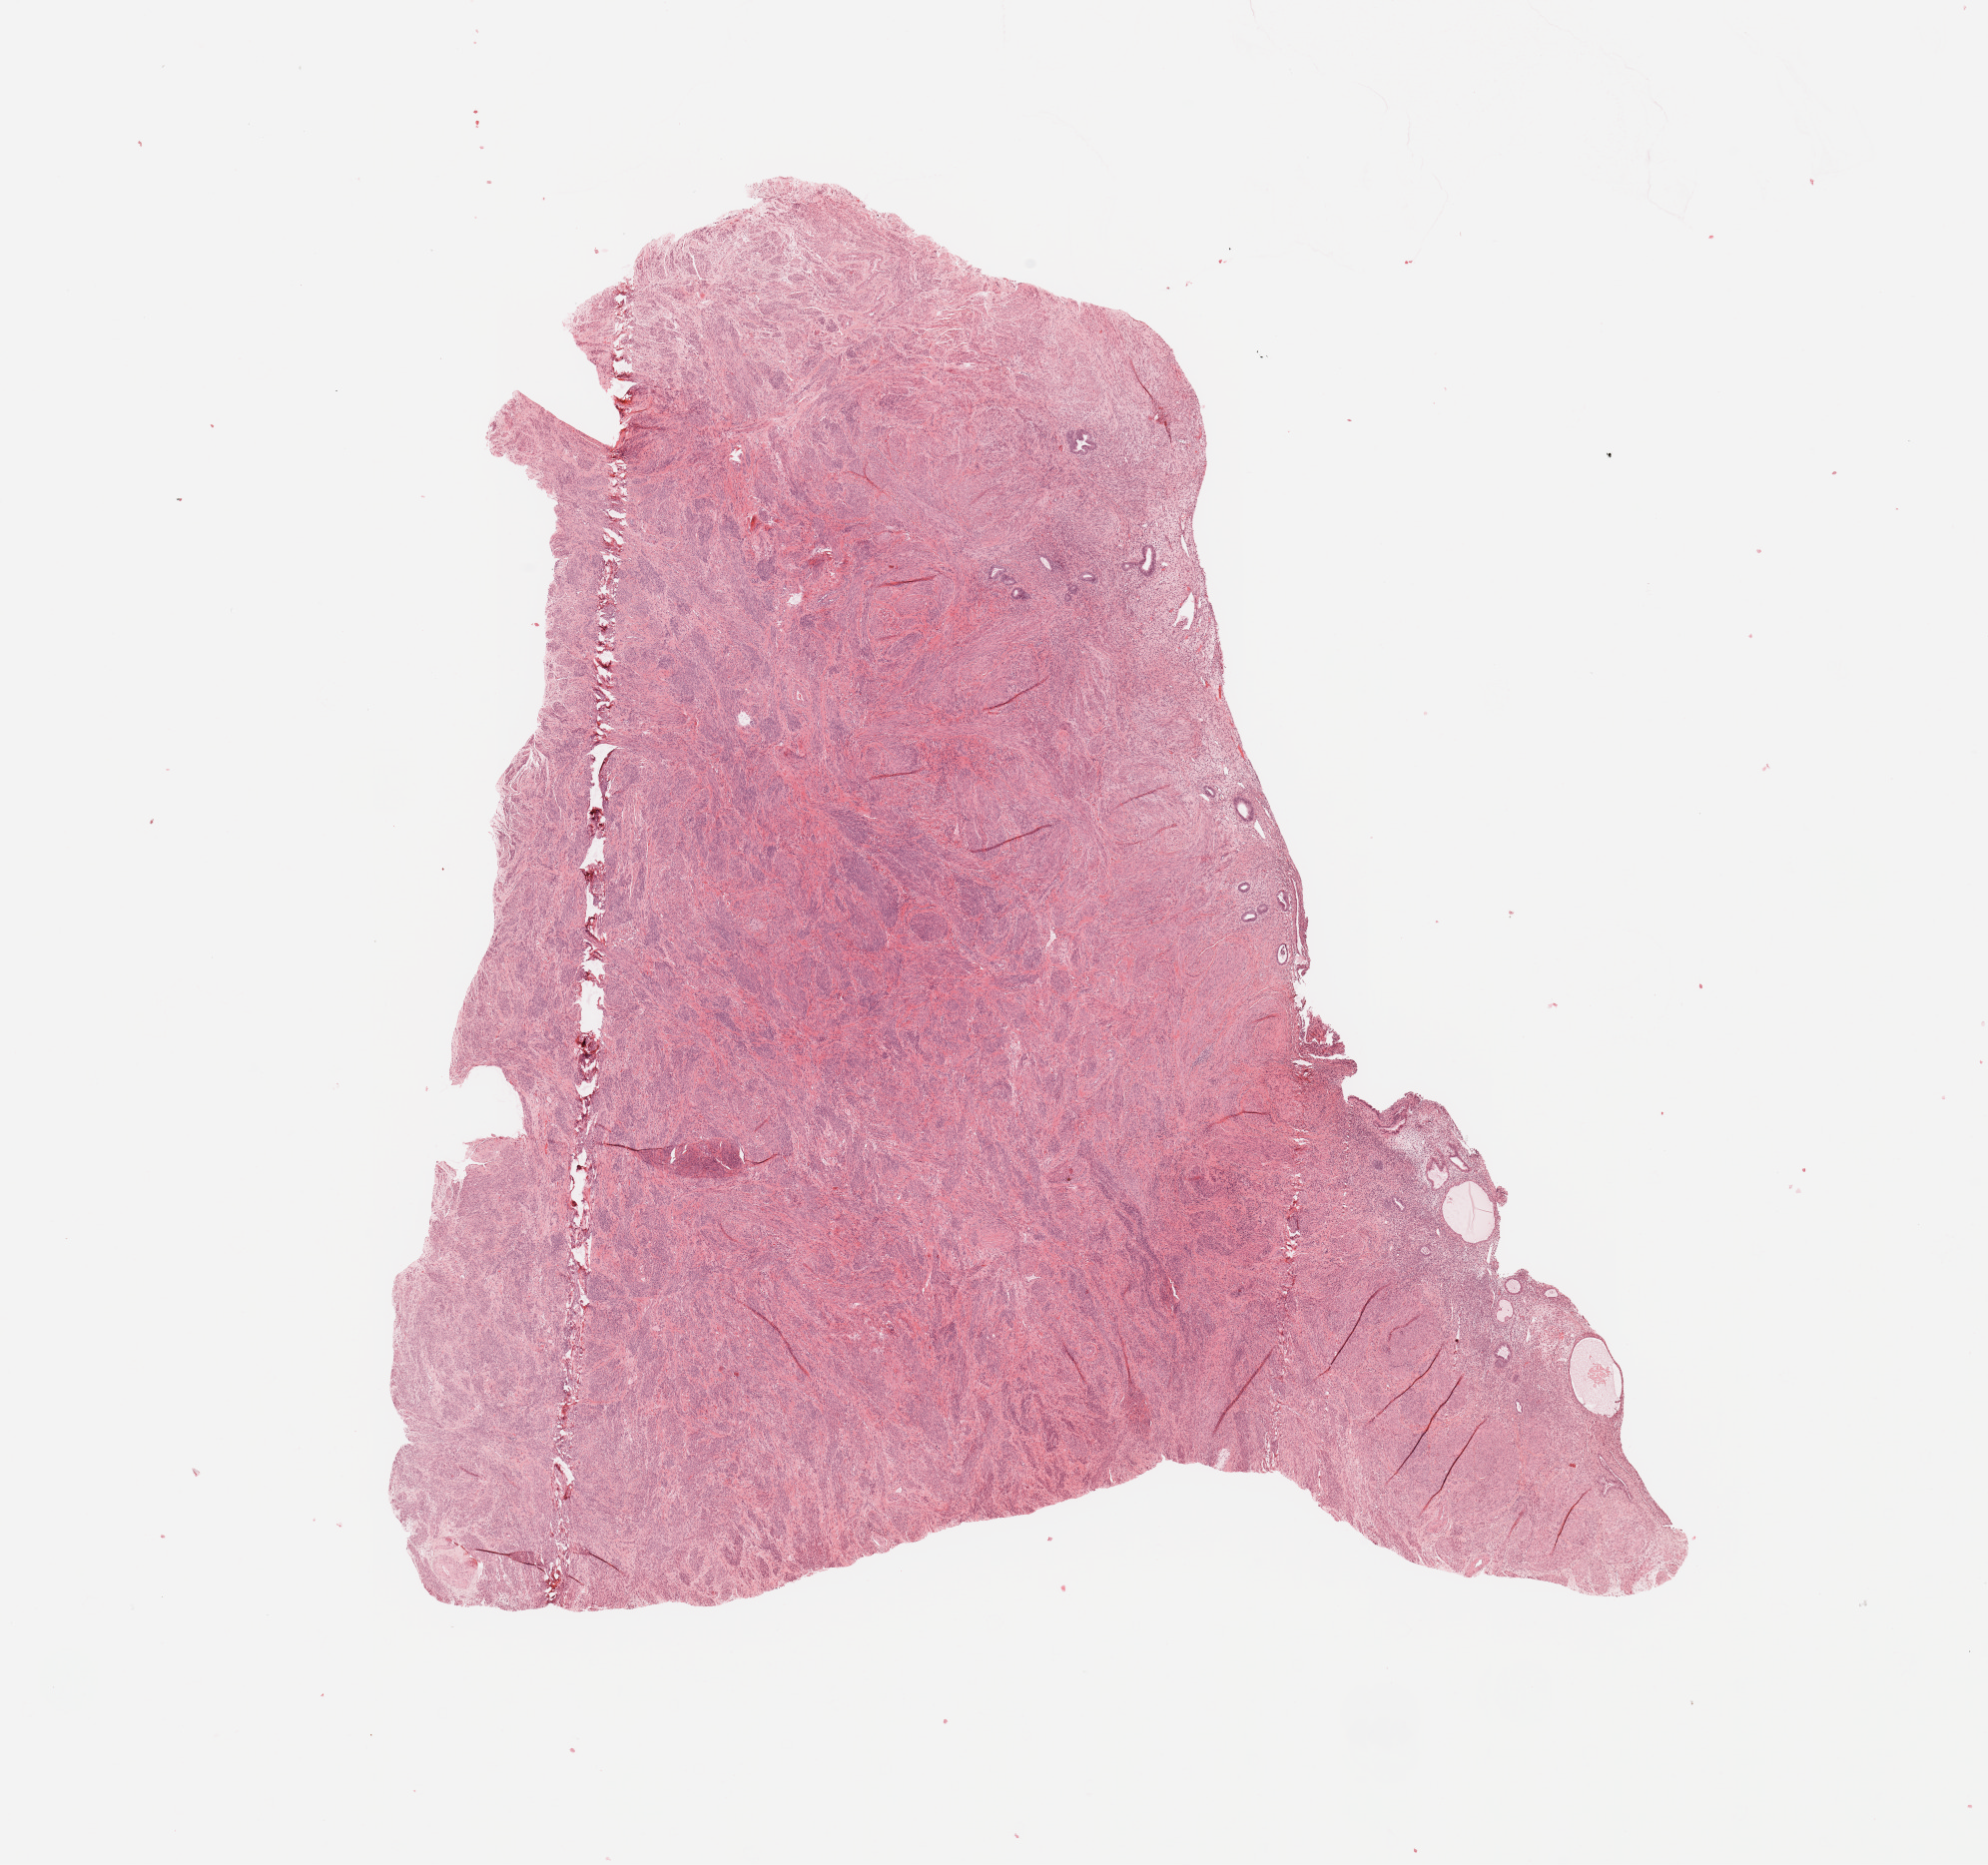
Digitized Hematoxylin and eosin (H&E) stained tissue section (whole slide) — a low-resolution overview of the entire scanned area, about 15.8 x 14.8 mm; uterus, normal (non-tumour) tissue. Female, 75 y/o.
This section: normal (non-tumour) tissue from the same patient. Patient diagnosis: Endometrioid adenocarcinoma, NOS.